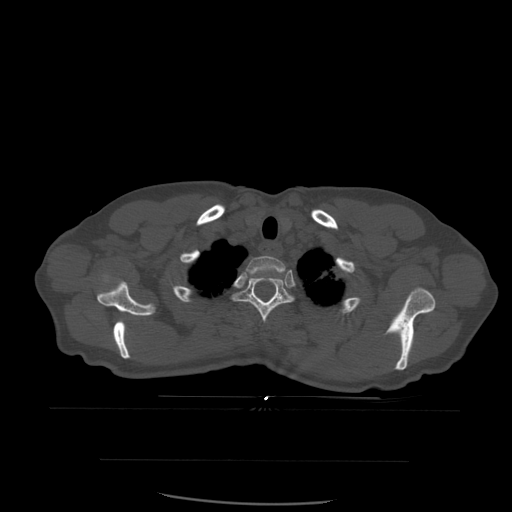
CT including the spine, one axial slice. Bone window (W 1800 / L 400 HU). 512 × 512 image matrix. Patient age 48 years. Case-level facts recorded for this patient, not image findings: primary cancer: lung; vertebrae with lytic lesions (as recorded): T11.
Outlined on this slice (semi-automatic segmentation, software-assisted and operator-edited):
- T1 vertebra: bounding box <248,256,286,279> (left, top, right, bottom; pixels)
- T2 vertebra: <232,271,294,324>